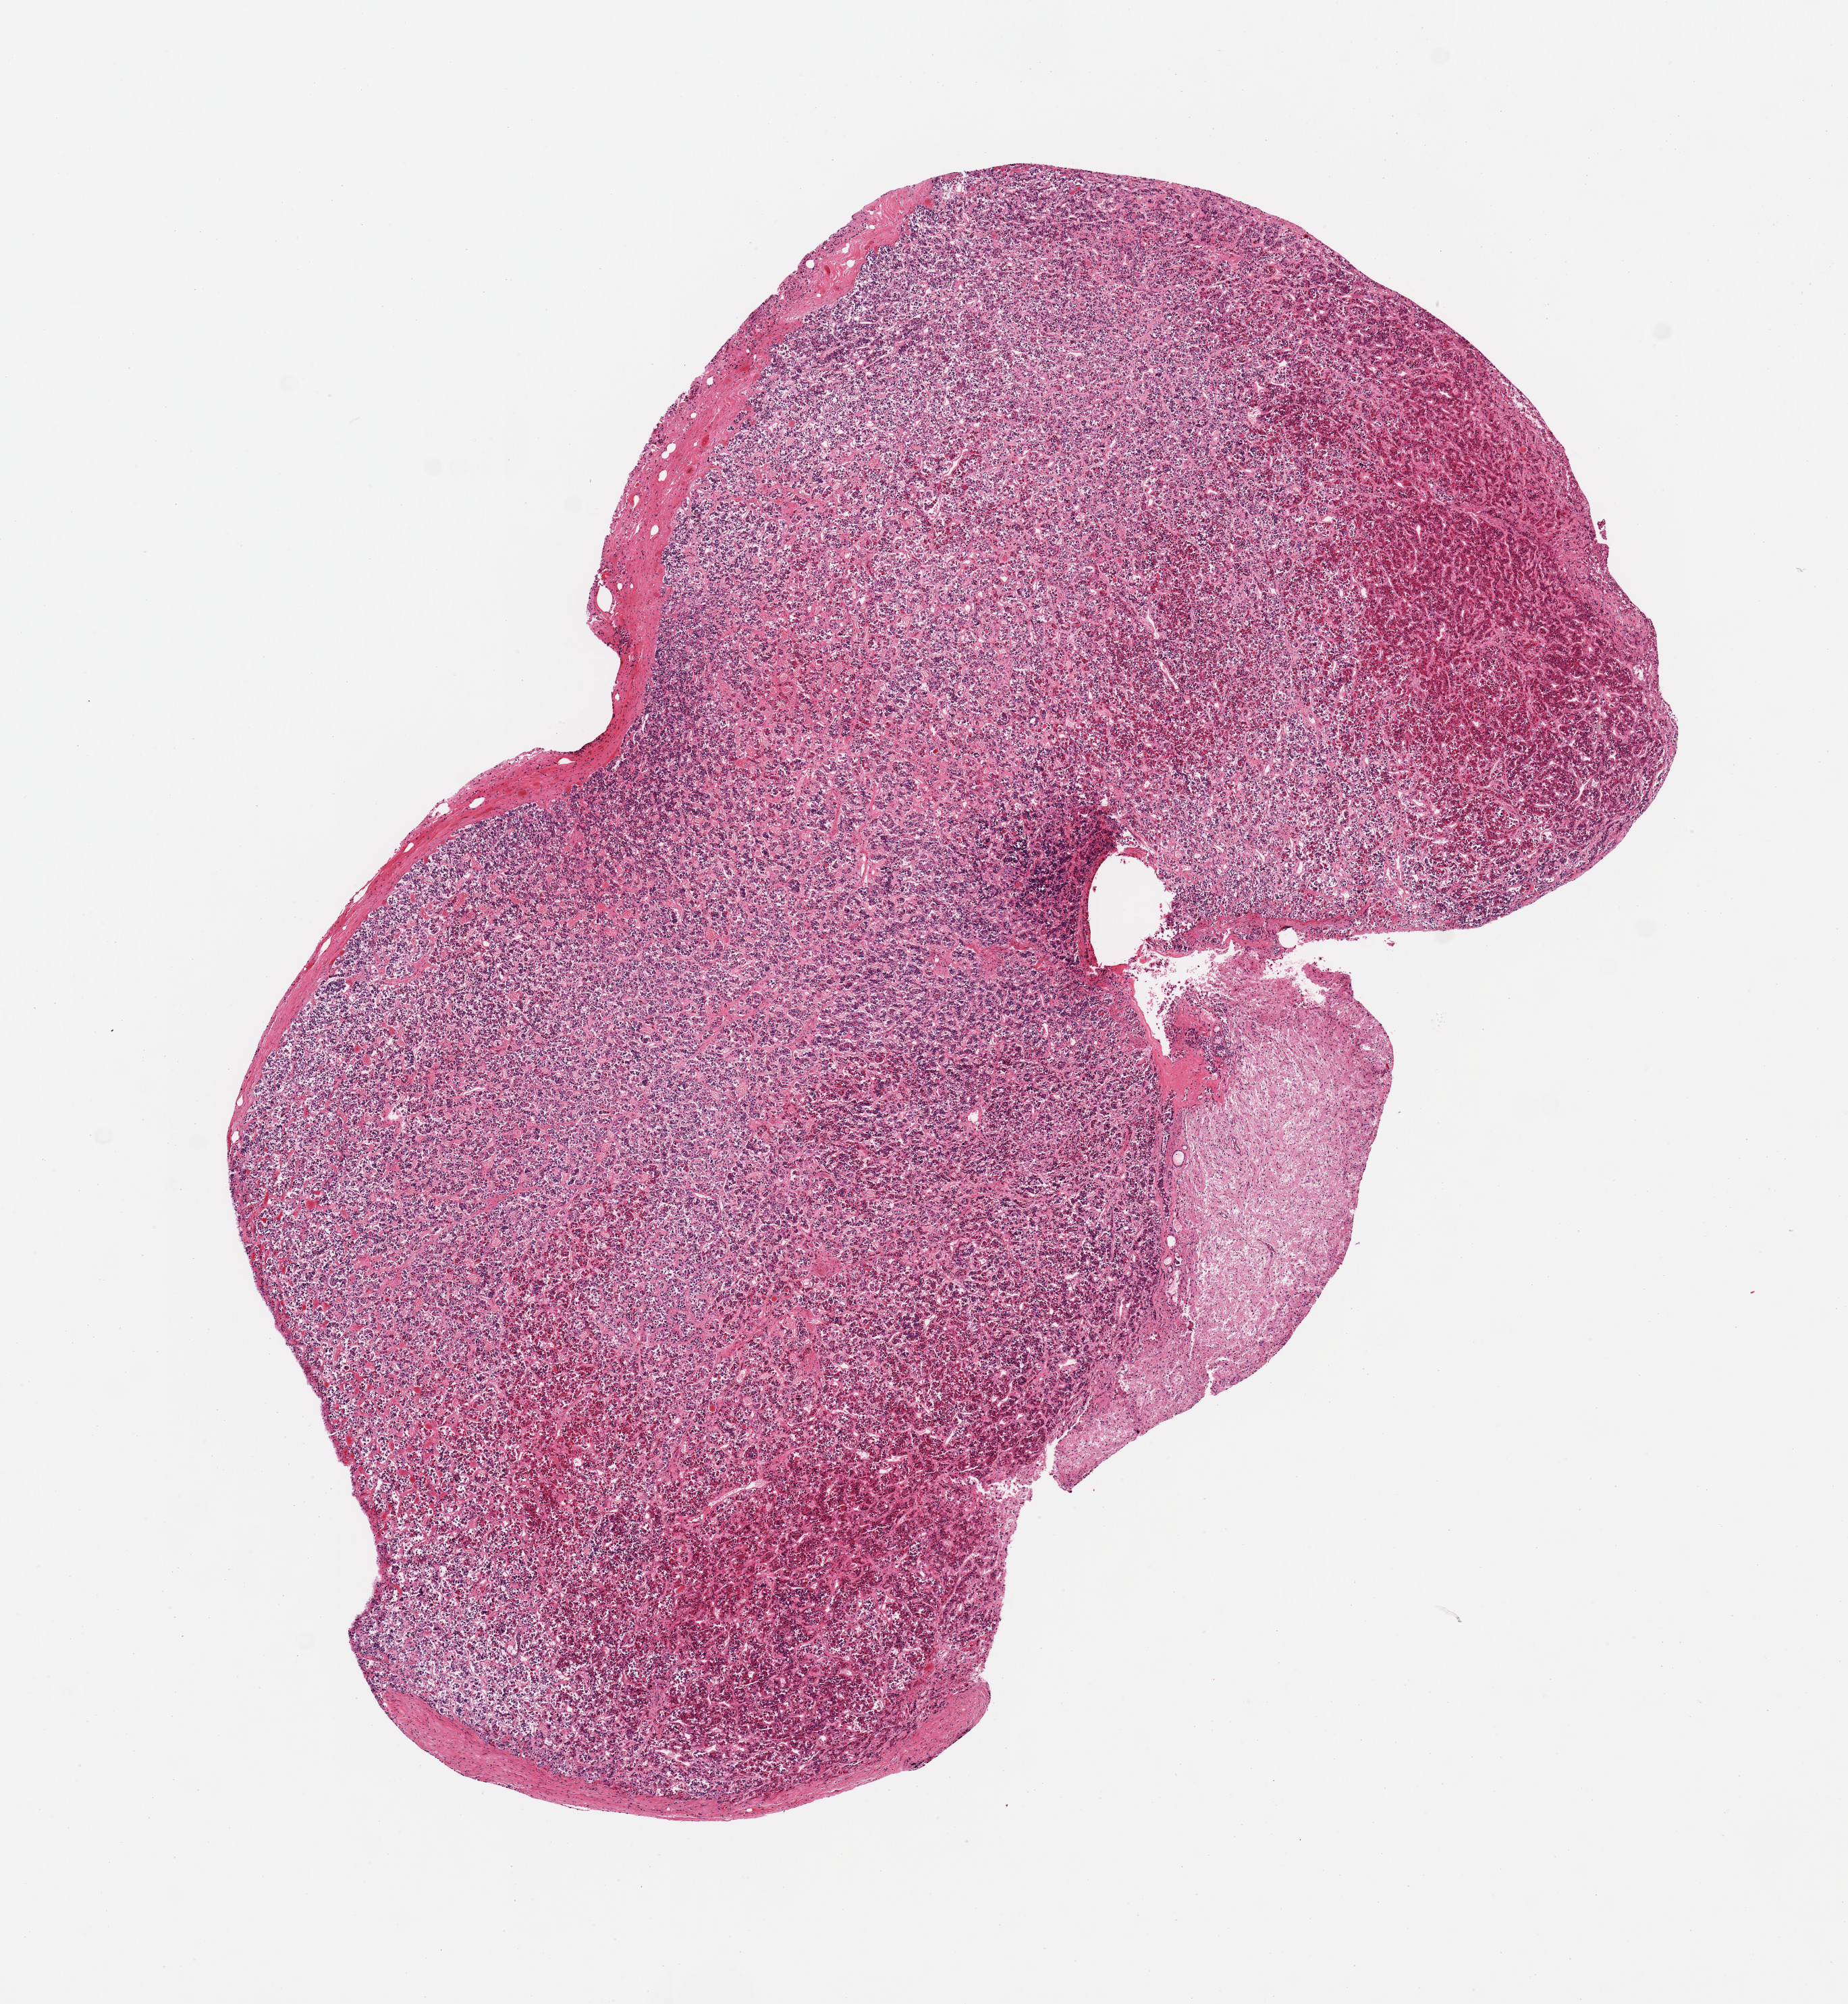
Digitized hematoxylin and eosin (H&E)-stained section, brightfield — shown as a low-resolution overview of the whole scanned area (about 10.8 x 11.7 mm); PAXgene-fixed, paraffin-embedded tissue; target tissue: pituitary; donor tissue sample. Male donor.
- pathologist's review note for this sample: 1 piece, ~3x1mm nubbin of neurohypophysis; rest is adenohypophysis